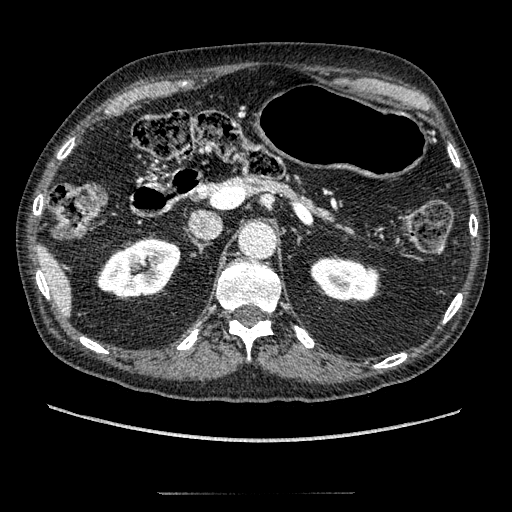
Contrast-enhanced abdominal CT, one axial slice; position 133 of 274 along the scan axis; reconstruction kernel STANDARD; 120 kVp; intravenous contrast given; soft-tissue window (W 400 / L 40 HU); 512 × 512 image matrix, field of view 381 × 381 mm. Male patient, age 69 years. From the clinical record (not read from this slice): diagnosis: adrenocortical carcinoma; tumour side: left adrenal; tumour size at pathology: 6.1 cm; Ki-67 index: 10 %; stage (as recorded): 3.
Annotated regions visible in this slice (semi-automatically segmented with operator editing):
- mass: bounding box [x1, y1, x2, y2] px = [437, 378, 439, 380]